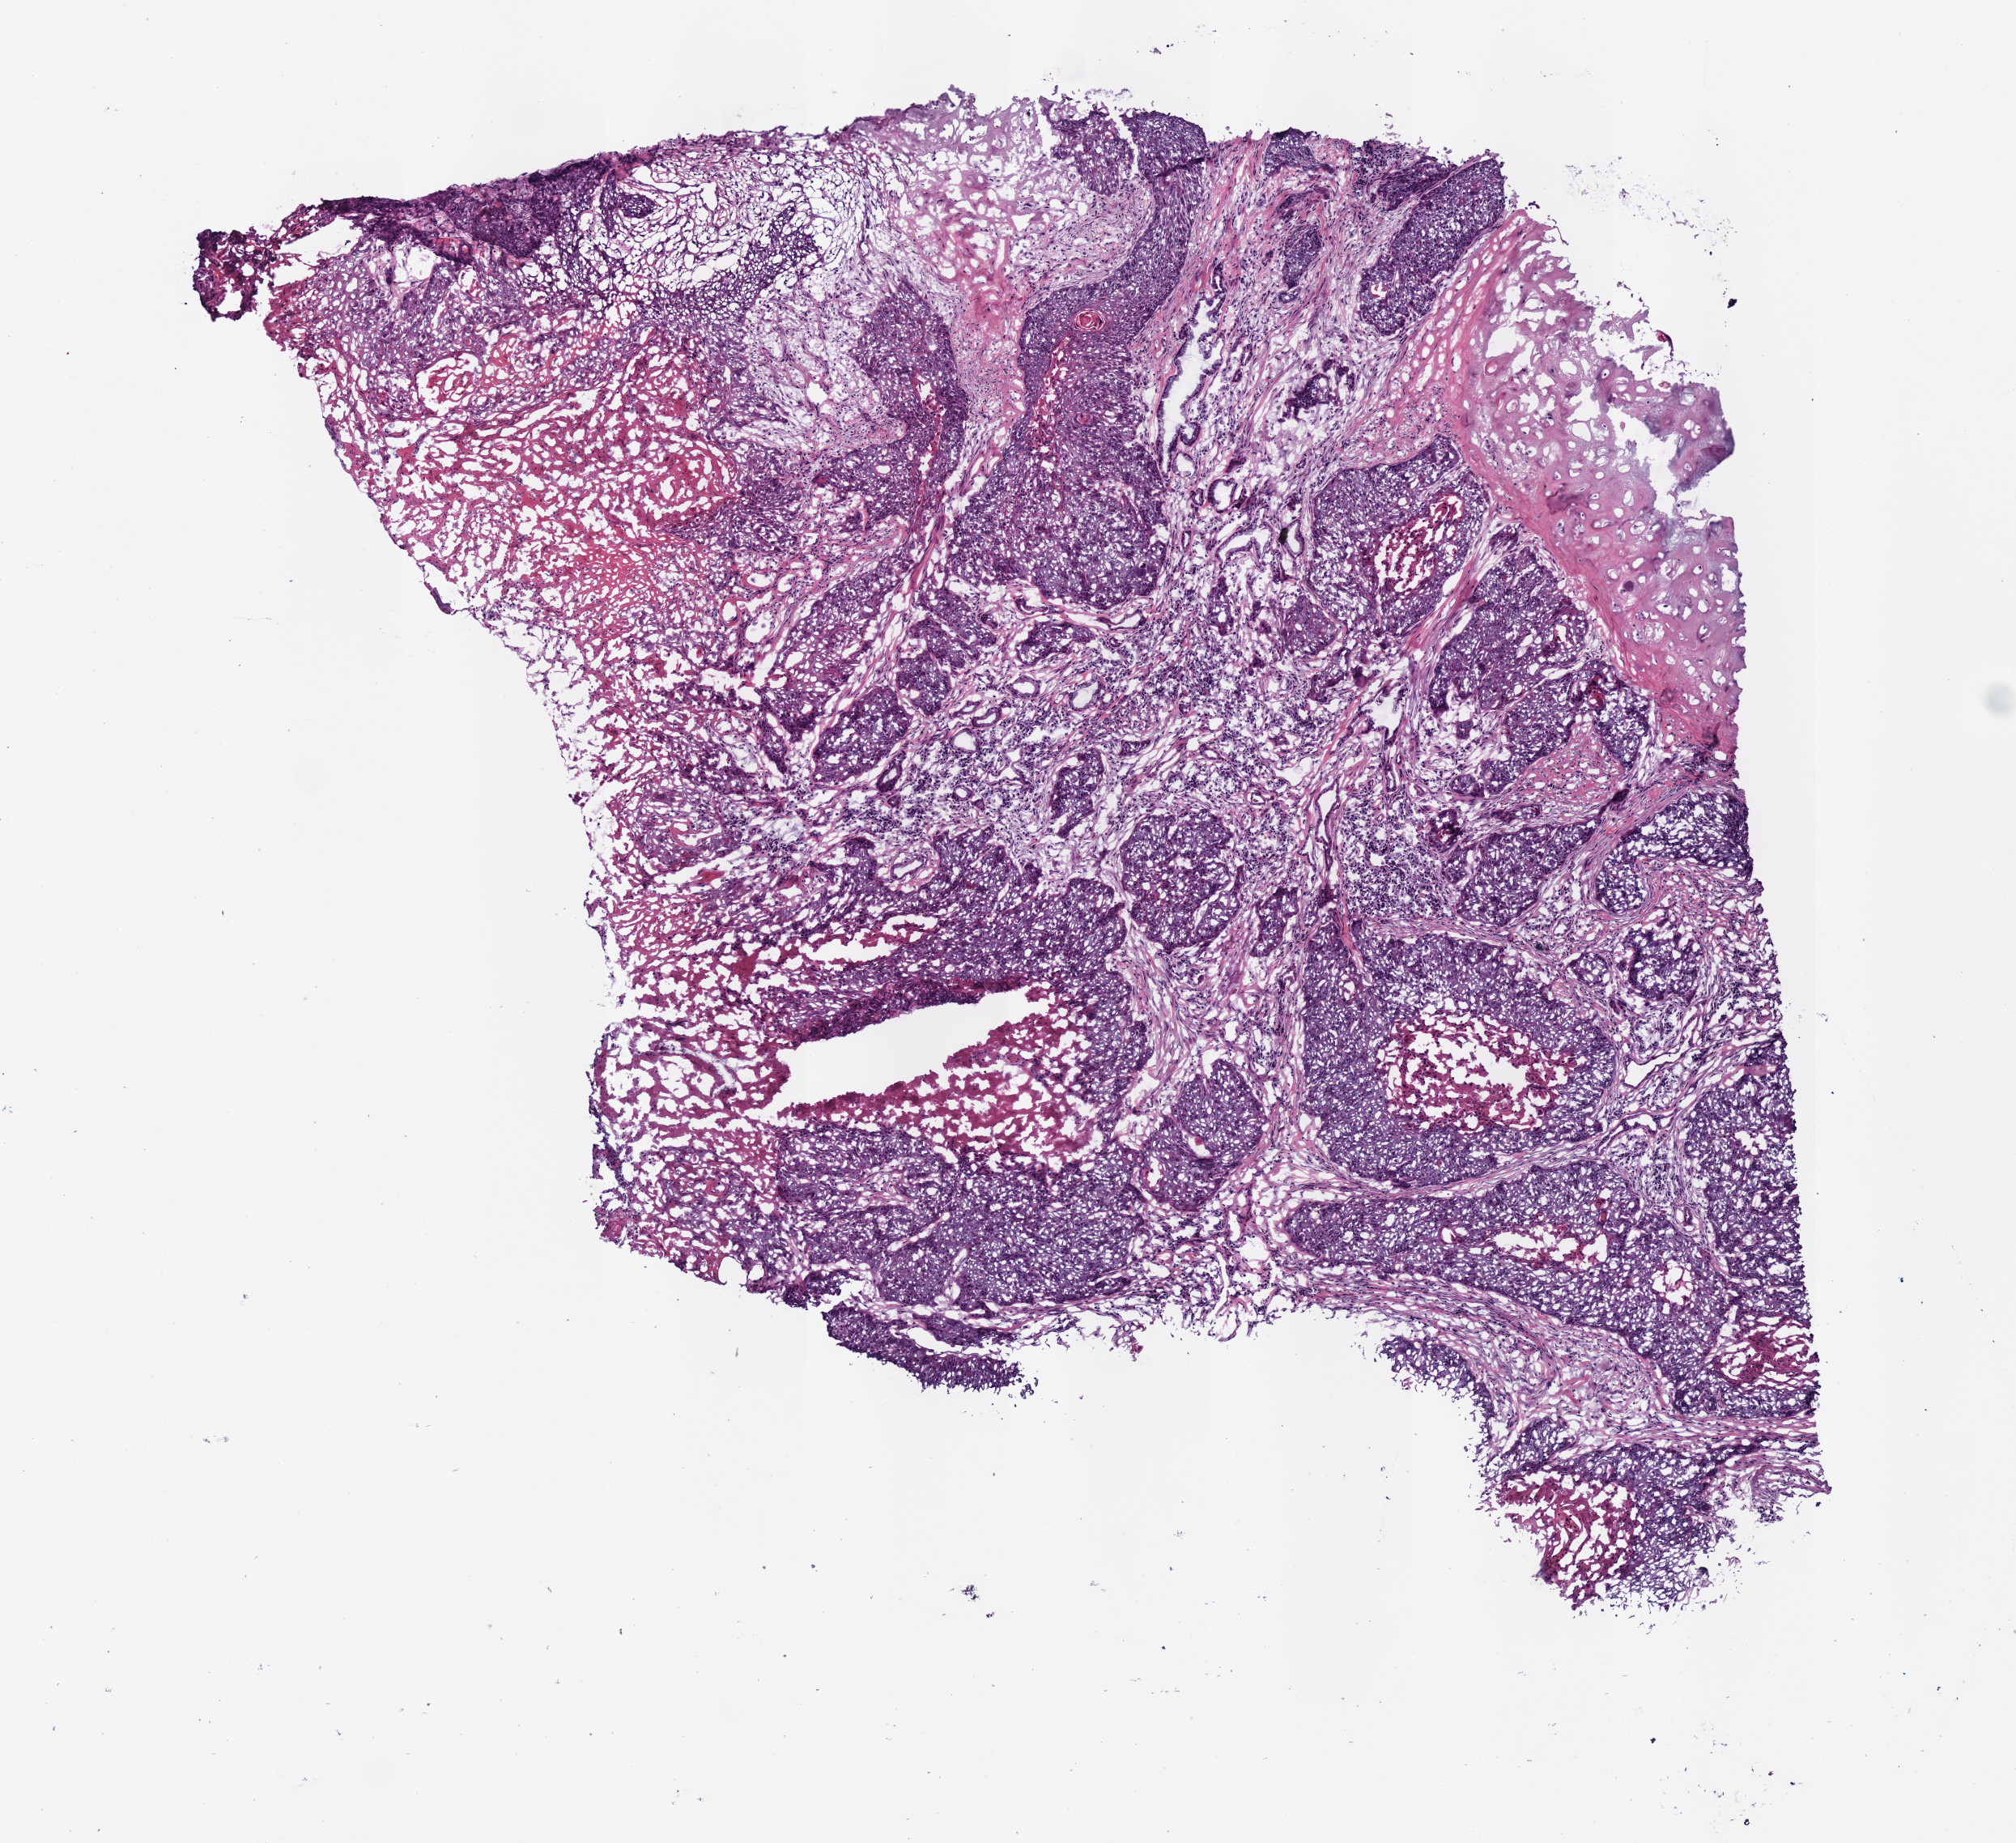
Whole-slide histology image, H&E-stained — low-resolution overview of the scanned area, about 4.9 x 4.5 mm. Frozen section. Primary tumour sample from the head and neck. Male patient; age at initial diagnosis 61 years. Histologic grade: G2 (moderately differentiated). Slide review estimates, as recorded: tumour cells 60%, tumour nuclei 70%, normal cells 5%, stromal cells 25%, necrosis 10%.
* diagnosis: Squamous cell carcinoma, NOS
* TNM: T2 N2c
* AJCC pathologic stage: IVA